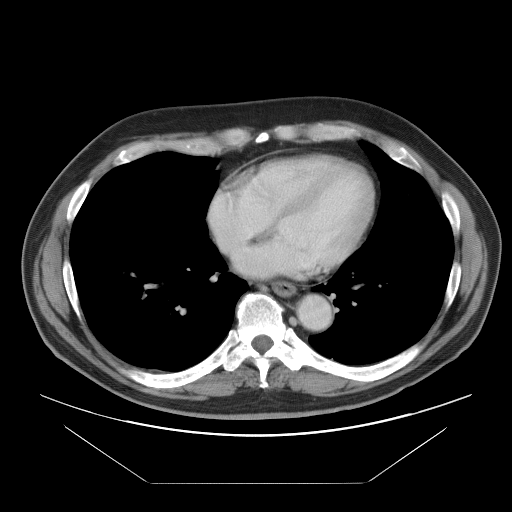
Contrast-enhanced abdominal CT, one axial slice. Intravenous contrast given. Soft-tissue window (W 400 / L 40 HU). 5 mm slice thickness. 512 × 512 image matrix, field of view 442 × 442 mm. Male patient, age 62 years. Case-level facts recorded for this patient, not image findings: diagnosis: colorectal cancer liver metastases, imaged before liver resection; multiple liver metastases: no; largest metastasis: 7 cm; disease in both lobes: yes.
Annotated regions visible in this slice (manually delineated by an expert):
- hepatic veins: bounding box (x1, y1, x2, y2) in pixels: (213, 199, 237, 262)